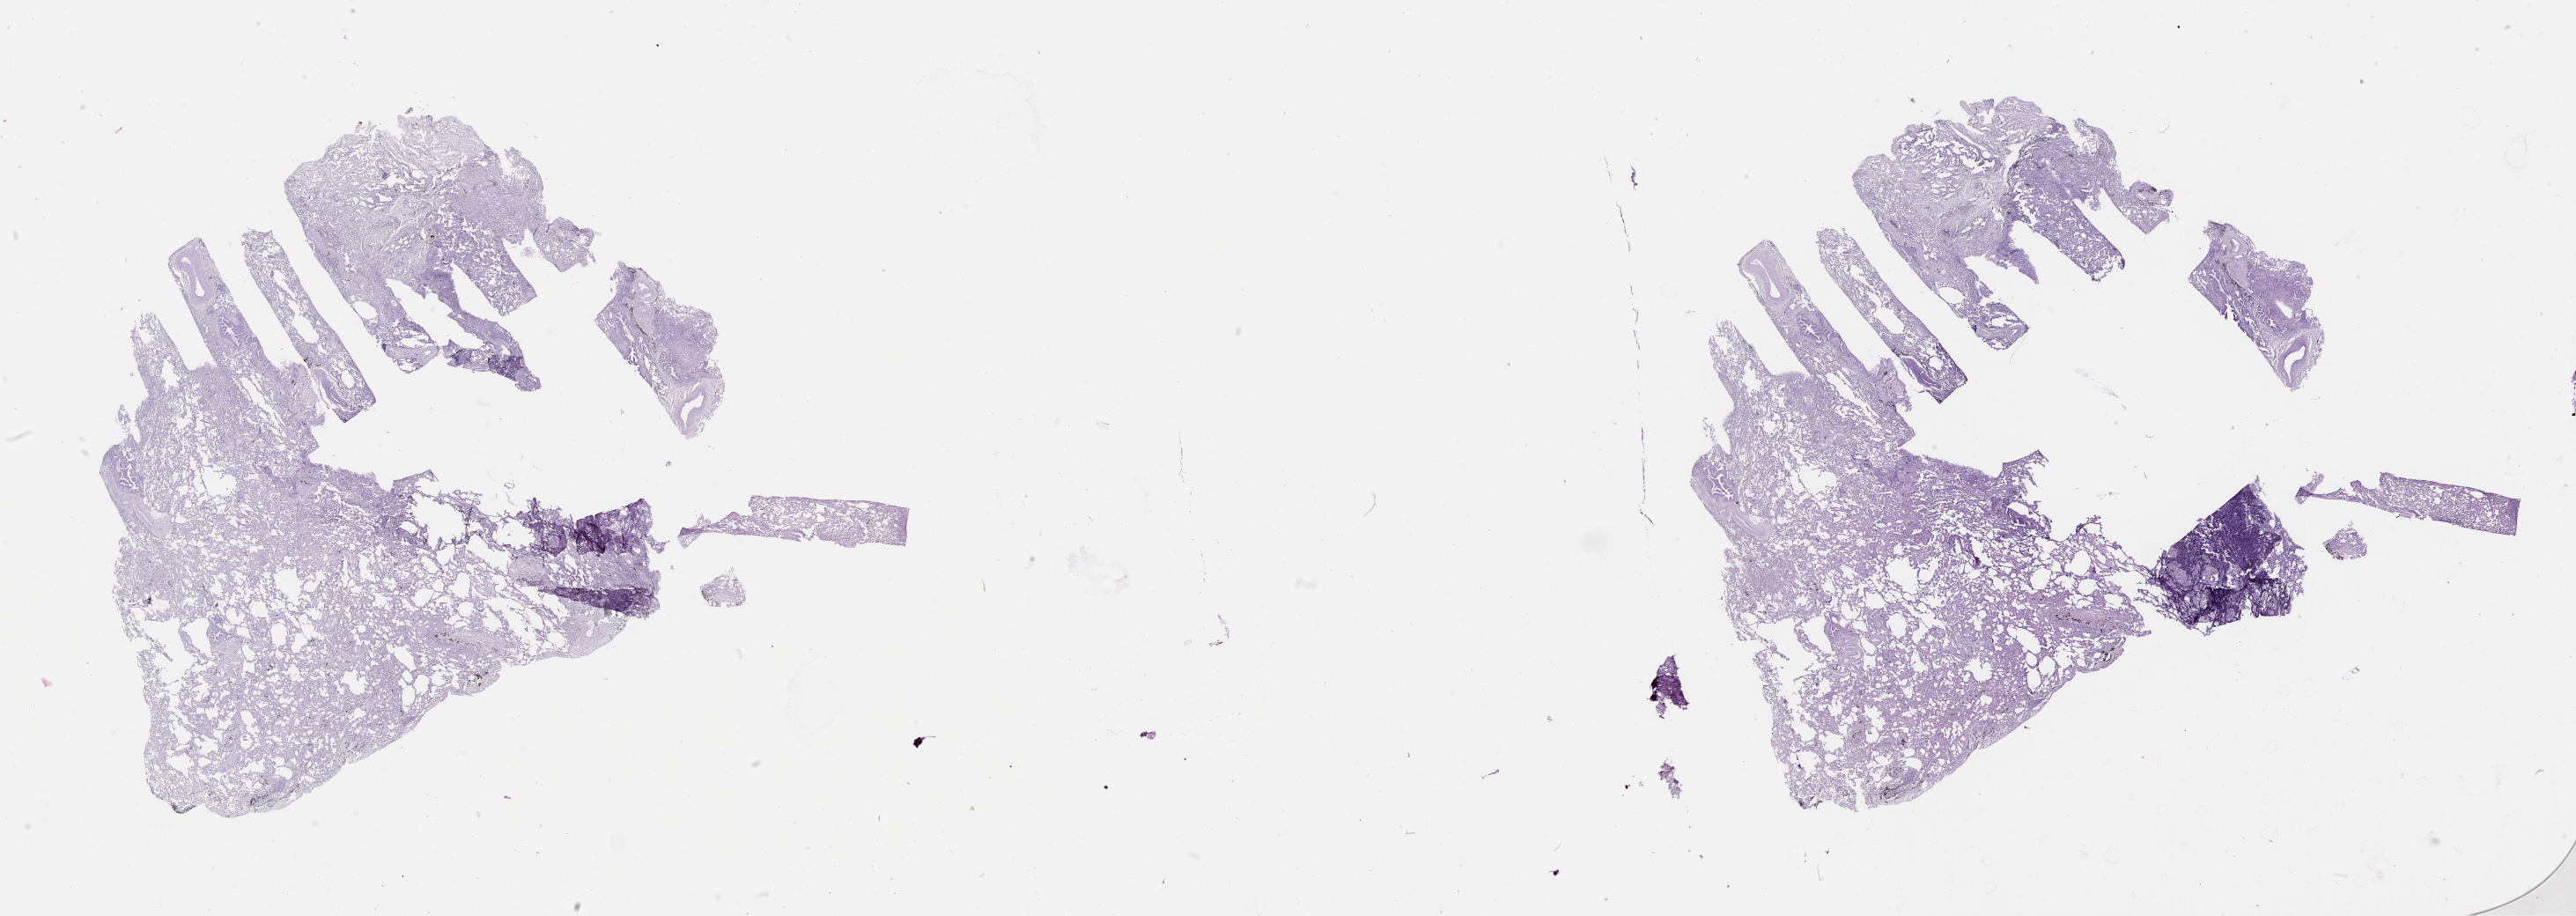
H&E whole-slide image — low-resolution overview of the scanned area, about 47.1 x 16.7 mm; normal (non-tumour) tissue sample, lung. Male, 70 y/o.
* this section: normal (non-tumour) tissue from the same patient
* patient diagnosis (cohort enrolment): squamous cell carcinoma (lung)